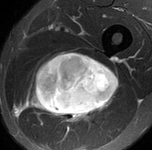
MRI of an extremity soft-tissue mass, one axial slice; slice 70 of 90 in the series (ordered by position); STIR; MR volume resampled by the dataset authors to the PET/CT grid (not the native acquisition matrix); 3.27 mm slice thickness; 152 × 150 image matrix. Male patient. From the clinical record (not read from this slice): histological type: undifferentiated pleomorphic liposarcoma; grade: high; site of the primary tumour: left thigh.
Structures marked on this image (expert contour drawn on MRI and transferred to this co-registered scan by the dataset authors):
- gross tumour volume including surrounding oedema: bounding box [x1, y1, x2, y2] px = [22, 53, 119, 125]
- gross tumour volume (mass): [32, 53, 119, 117]